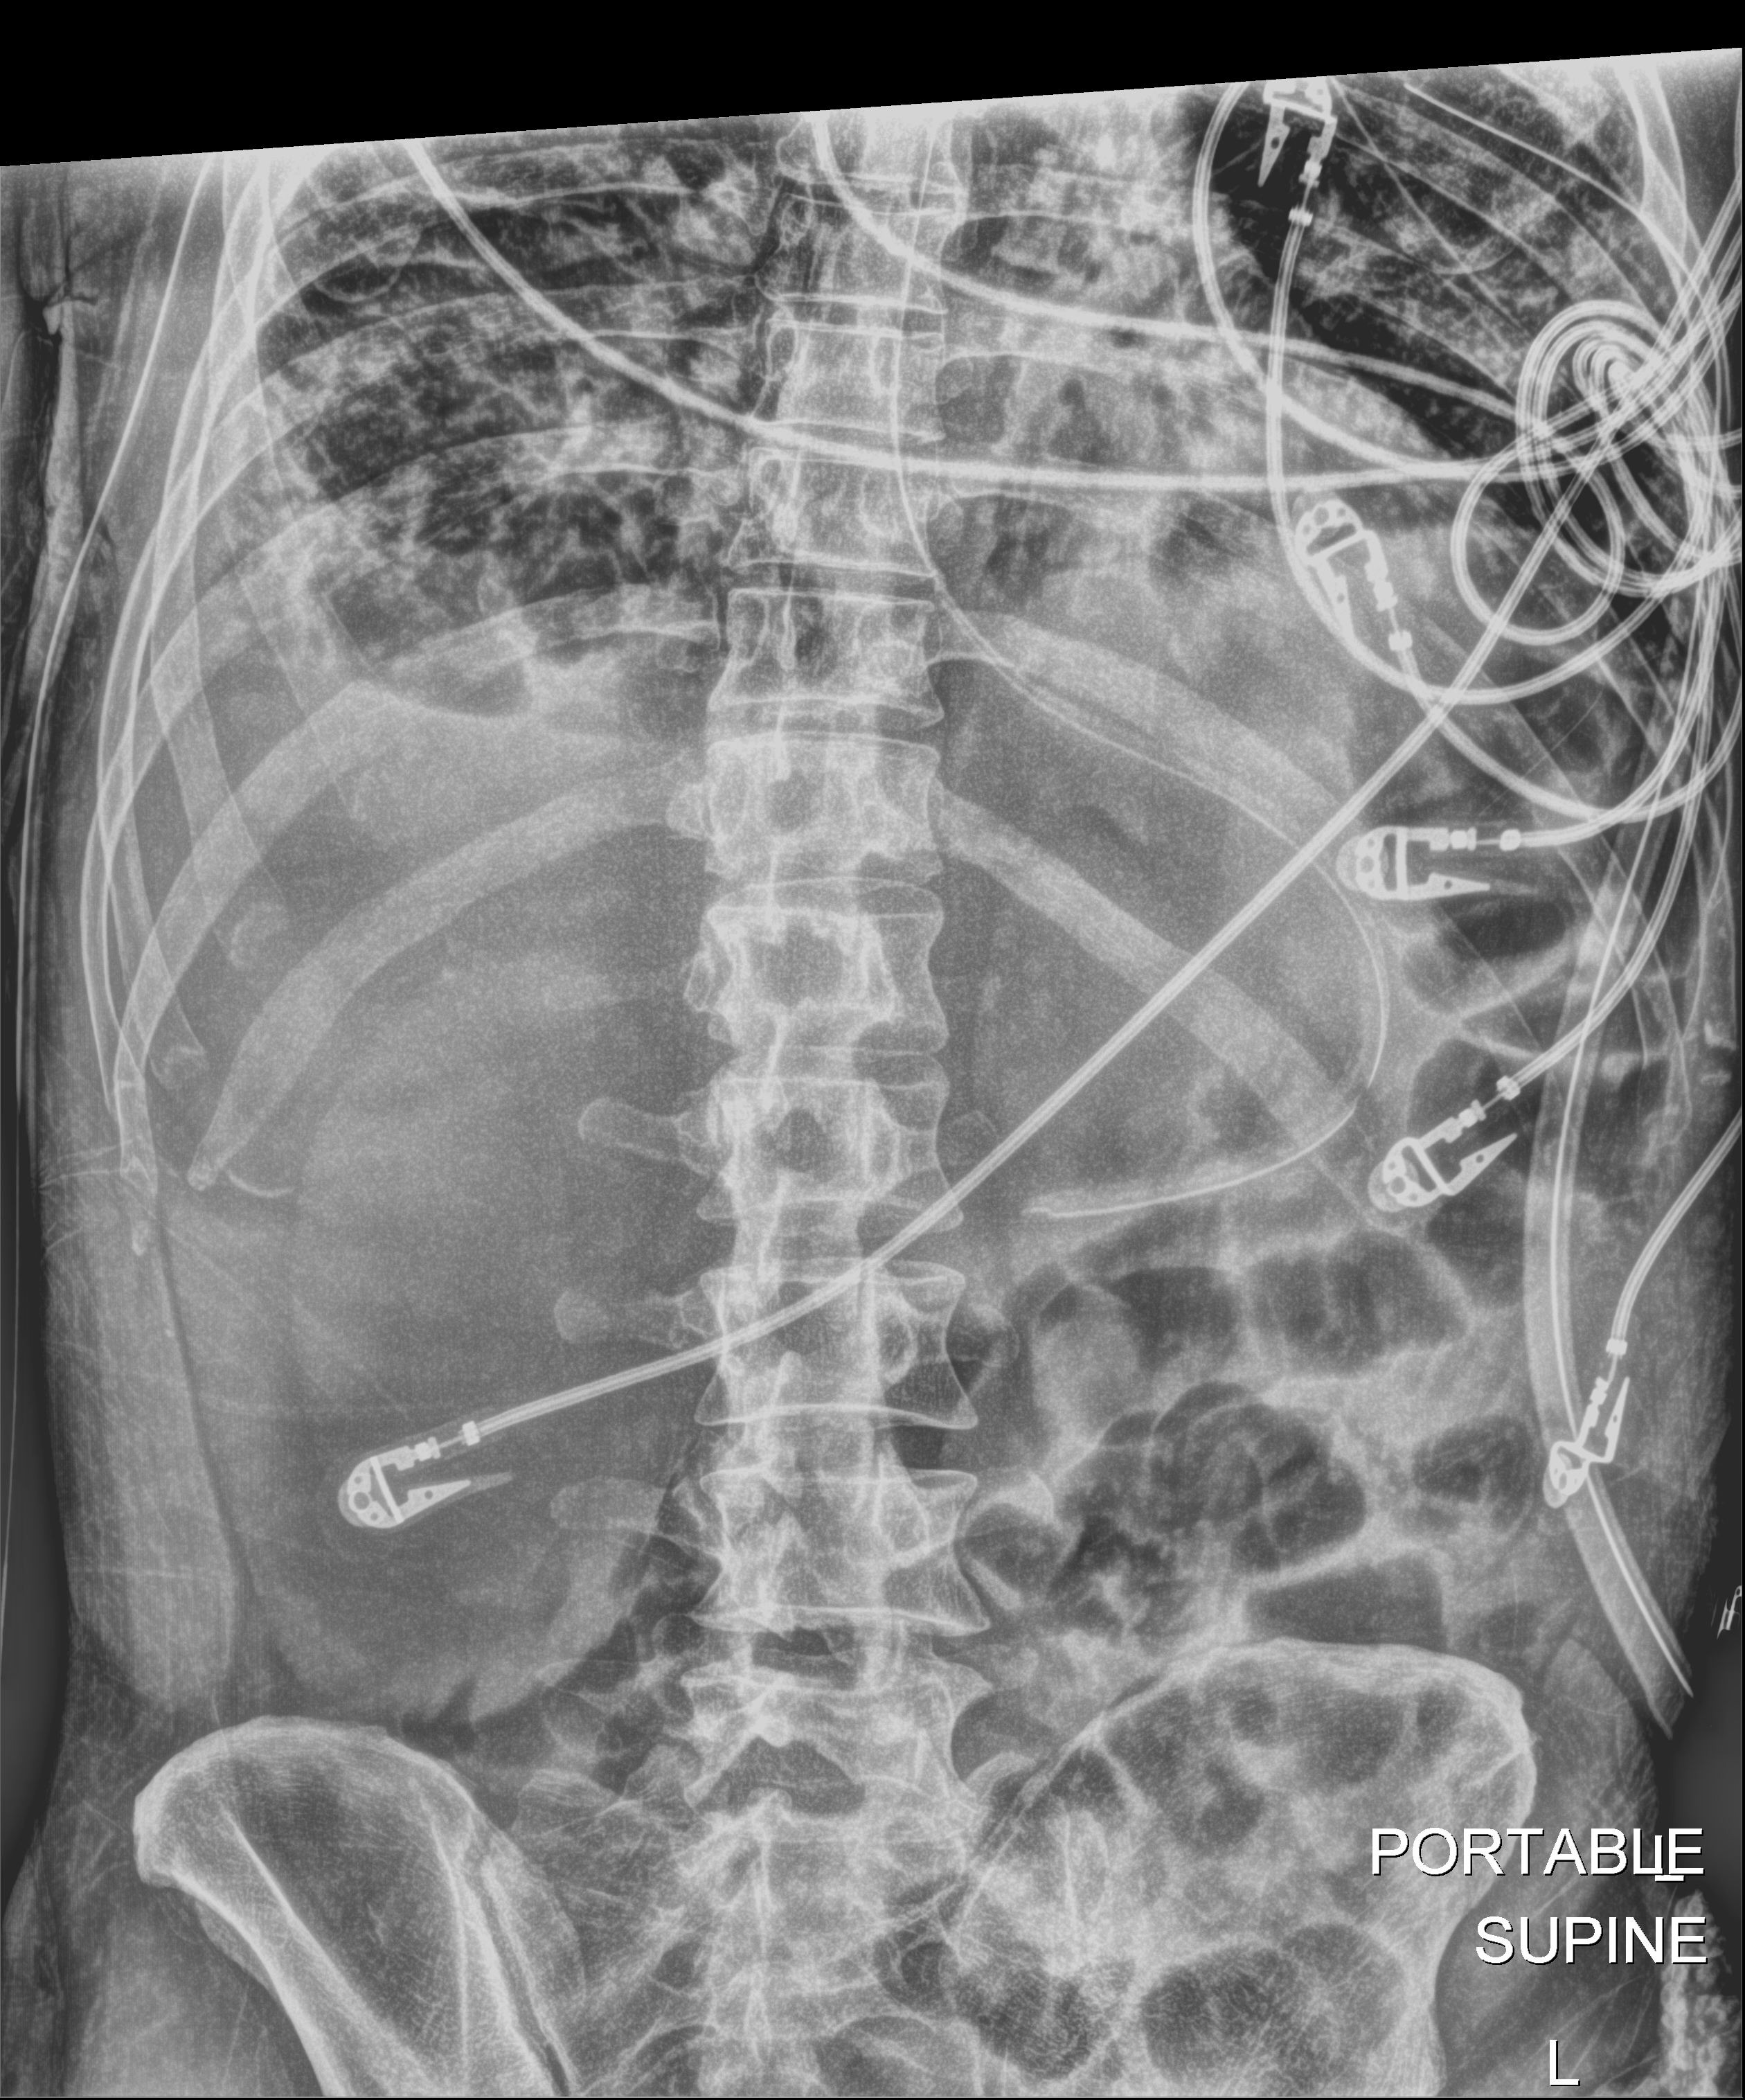
Bedside abdomen radiograph (digital radiography), anteroposterior (AP) projection. Patient hospitalised with COVID-19; male, aged 18–59 years.
Admission-level facts for this patient (not findings on this image; timing relative to this image not recorded):
- mechanically ventilated during this hospital stay: yes
- length of hospital stay: 96 days